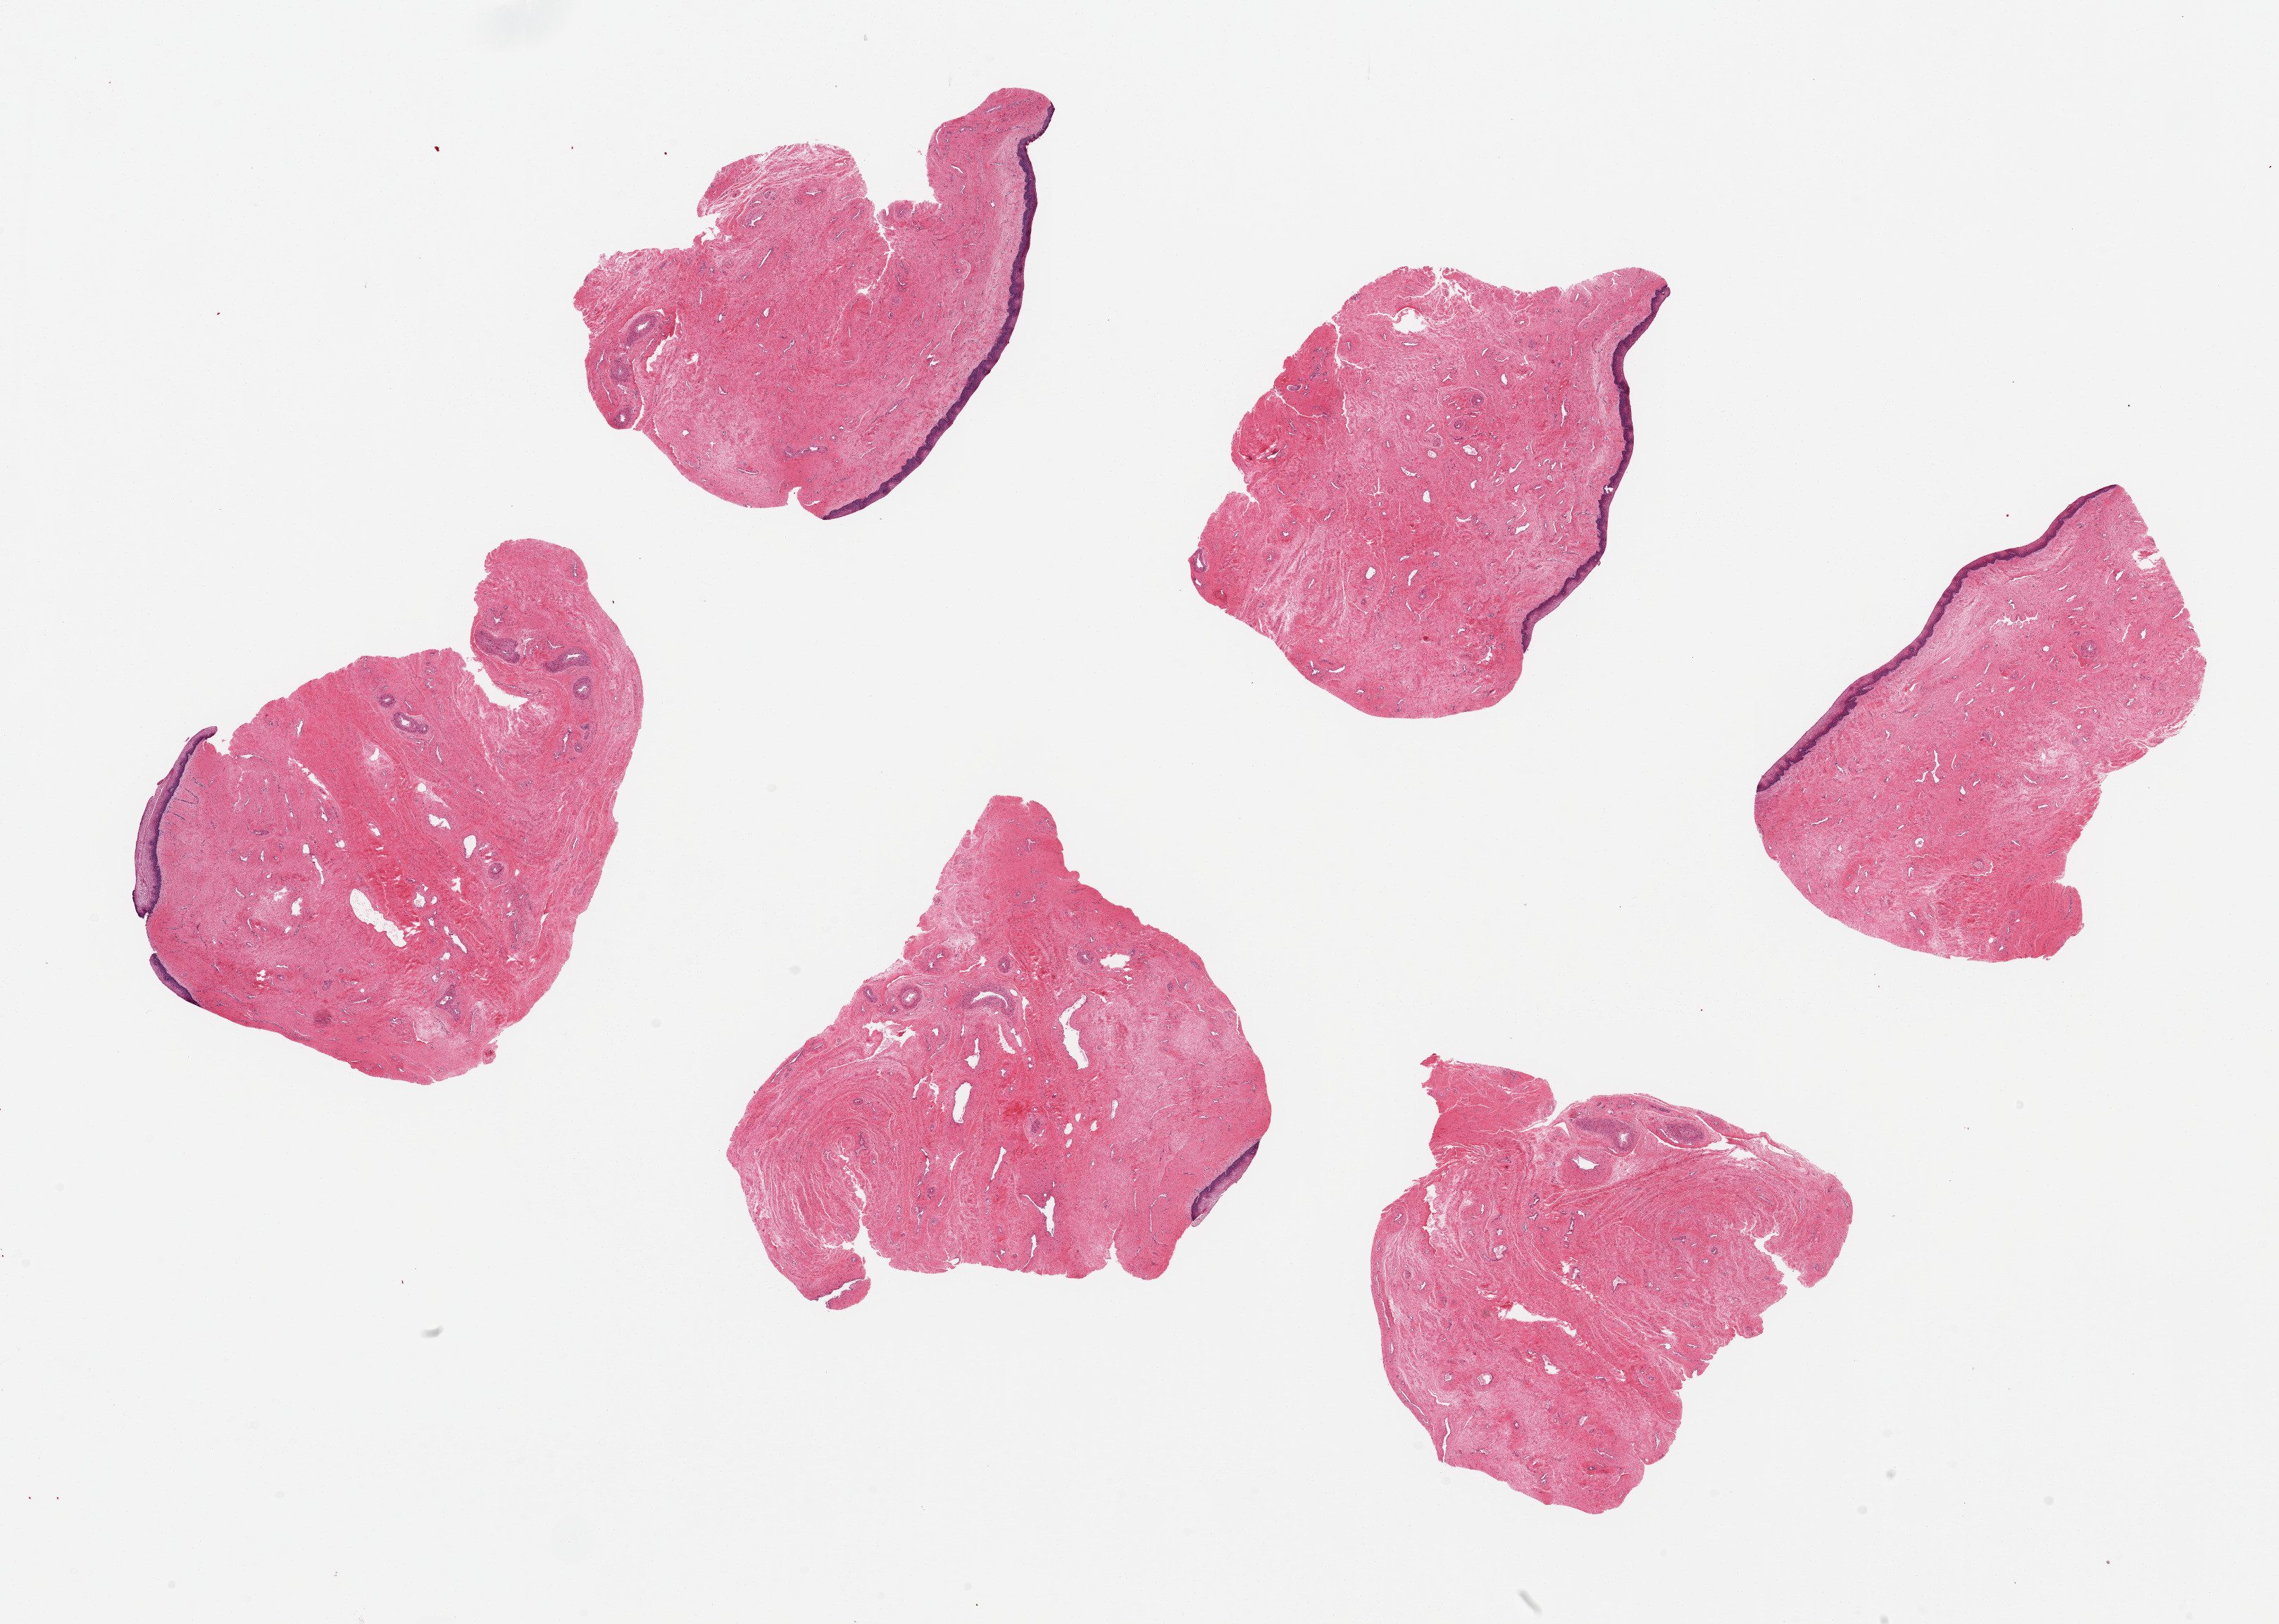
Digitized H&E-stained section, brightfield, shown as a low-resolution overview of the whole scanned area (about 25.6 x 18.2 mm, acquisition: 20x scan), PAXgene-fixed paraffin-embedded (PFPE) section, target tissue: vagina, tissue donor sample. Donor: female.
- review note (as recorded): 6 pieces, ~ 5x4mm, squamous mucosa is ~ 2-3% of thickness, present at least focally in 5 of 6 aliquots